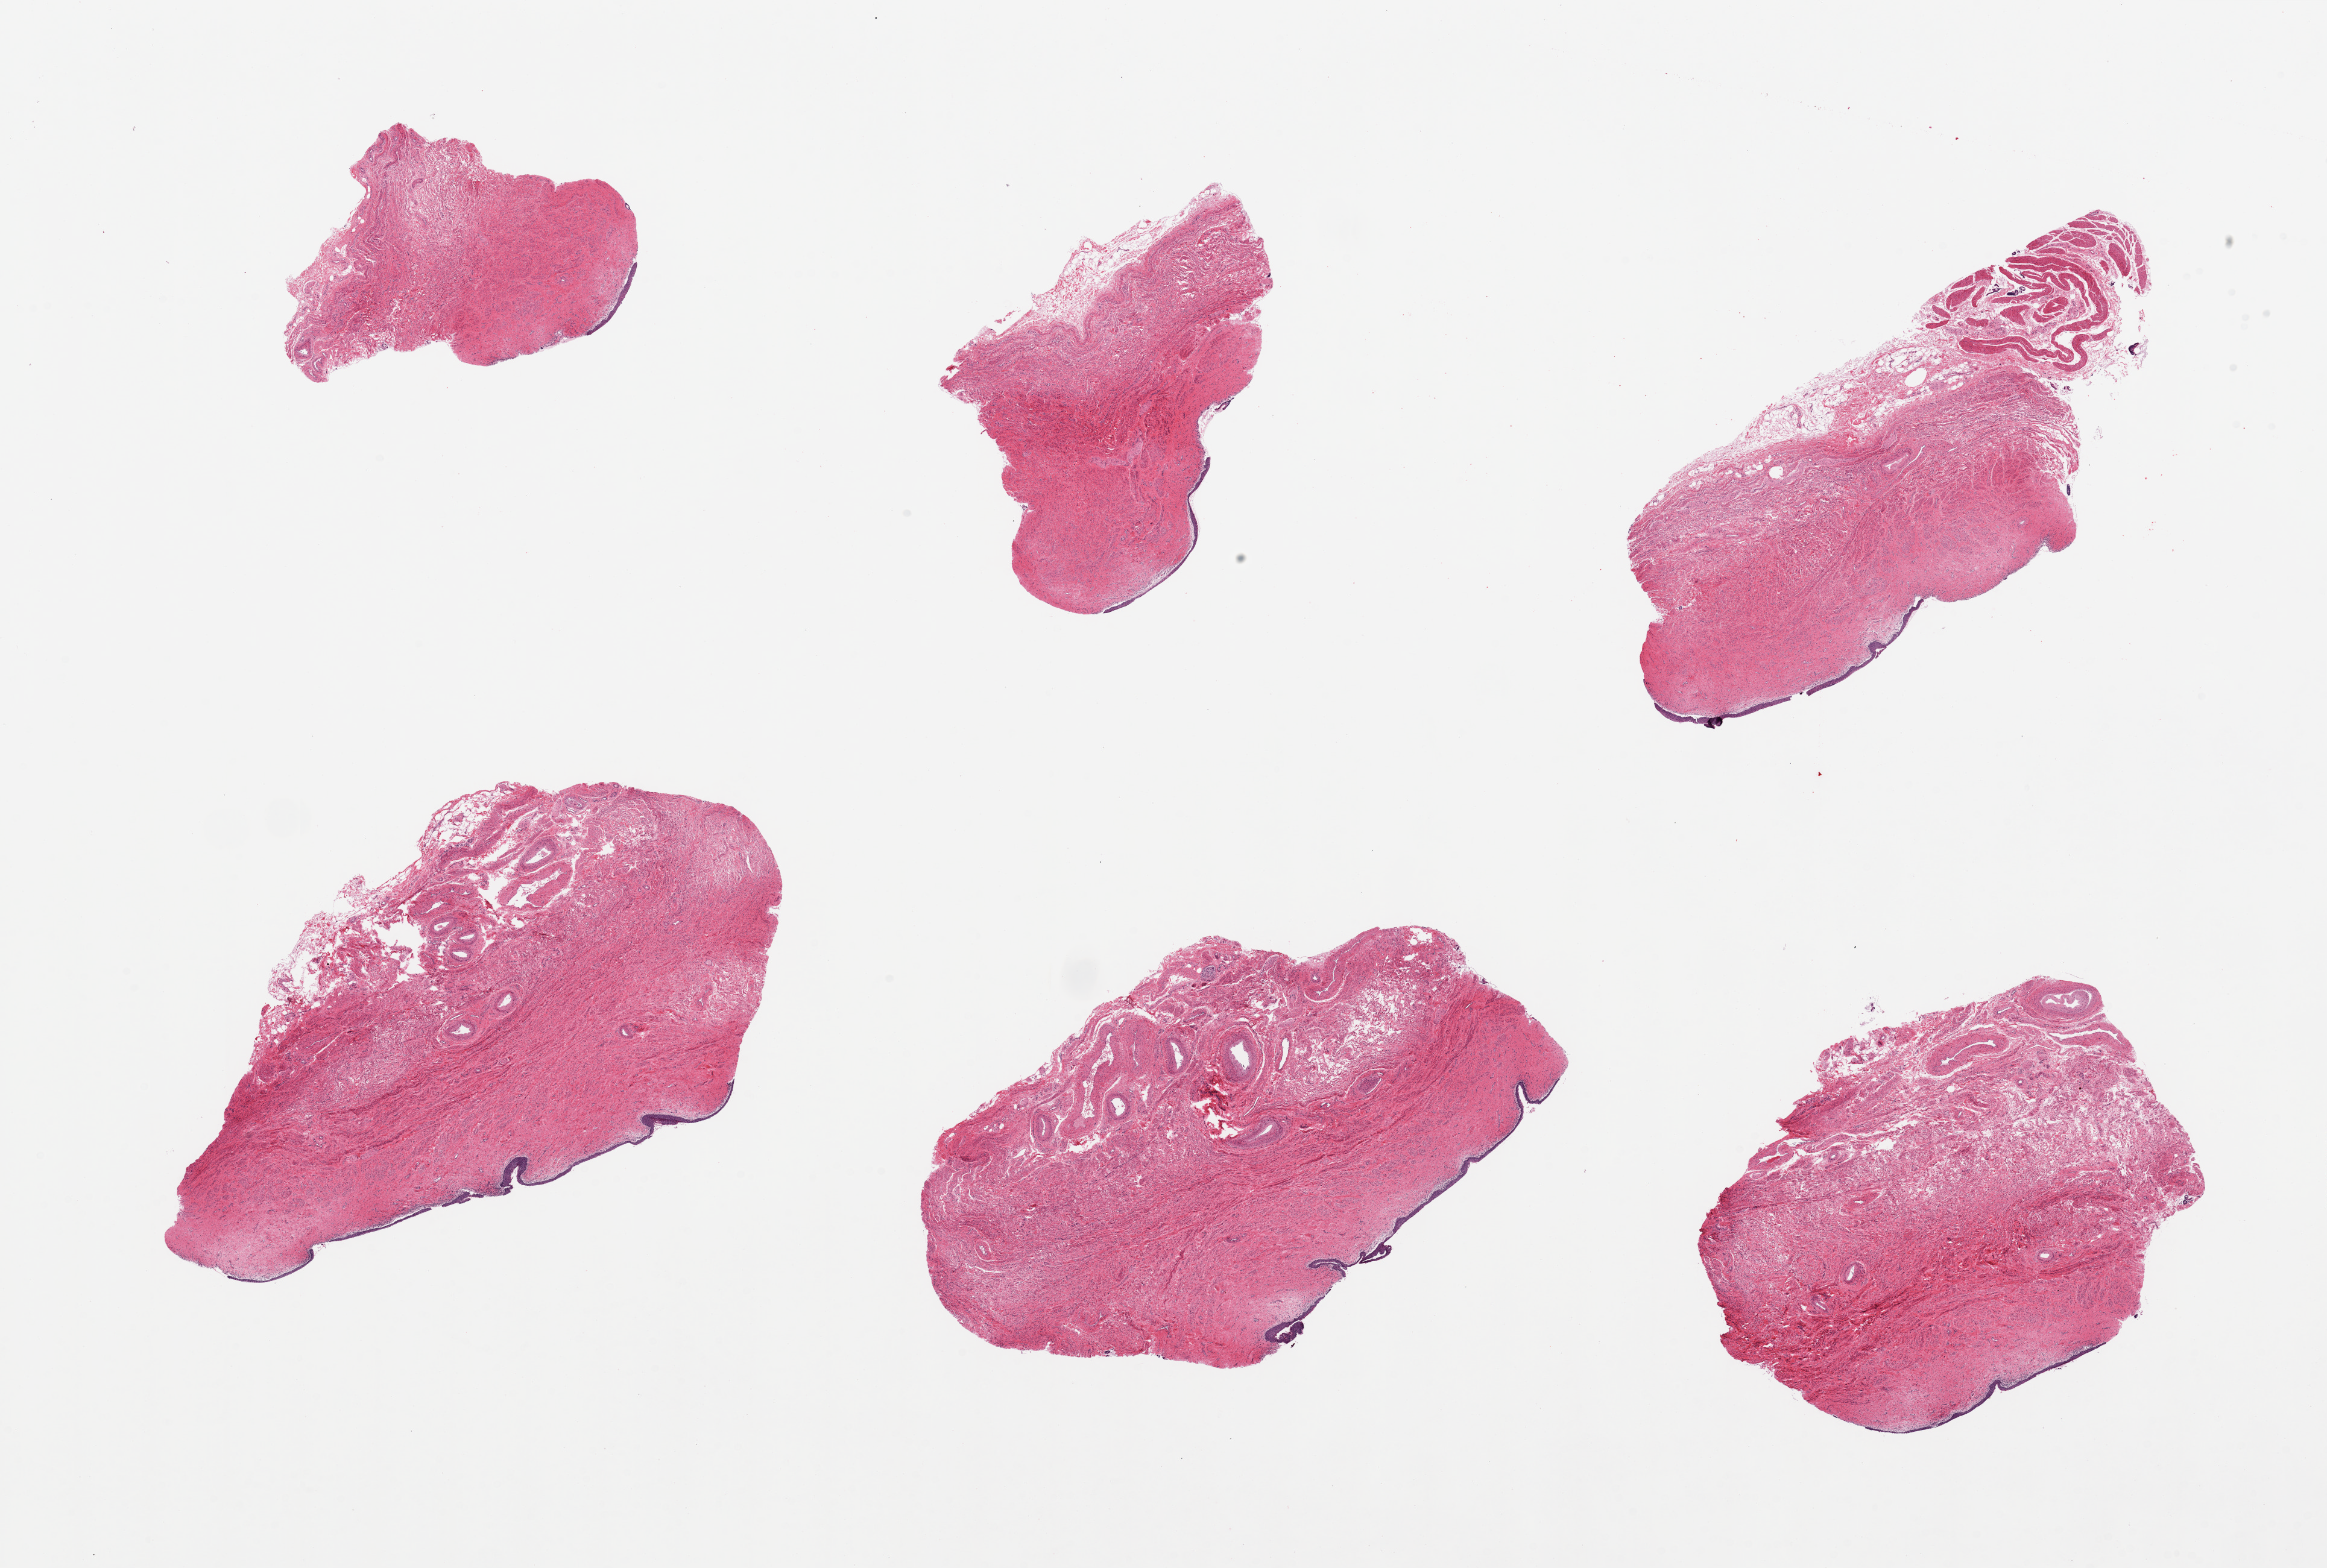
Haematoxylin and eosin whole-slide image, whole scanned area (about 30.5 x 20.6 mm) shown as a low-resolution overview, PAXgene-fixed paraffin-embedded (PFPE) section, sampled site (target tissue): vagina, donor tissue sample.
* review note (as recorded): 6 pieces, epithelium partly sloughed, several floaters (some)